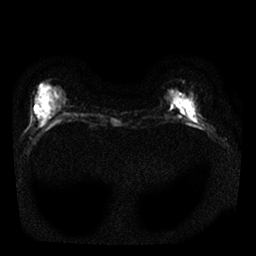
Breast MRI, one axial slice. Position 6 of 25 along the scan axis. Diffusion-weighted series; image 2 of 4 stored at this slice position (different b-values; order by instance number). 1.5 T. 4 mm slice thickness. 256 × 256 image matrix. Female patient.
Structures marked on this image (manually delineated by an expert):
- tumour on diffusion-weighted imaging: bounding box <181,110,184,113> (left, top, right, bottom; pixels)